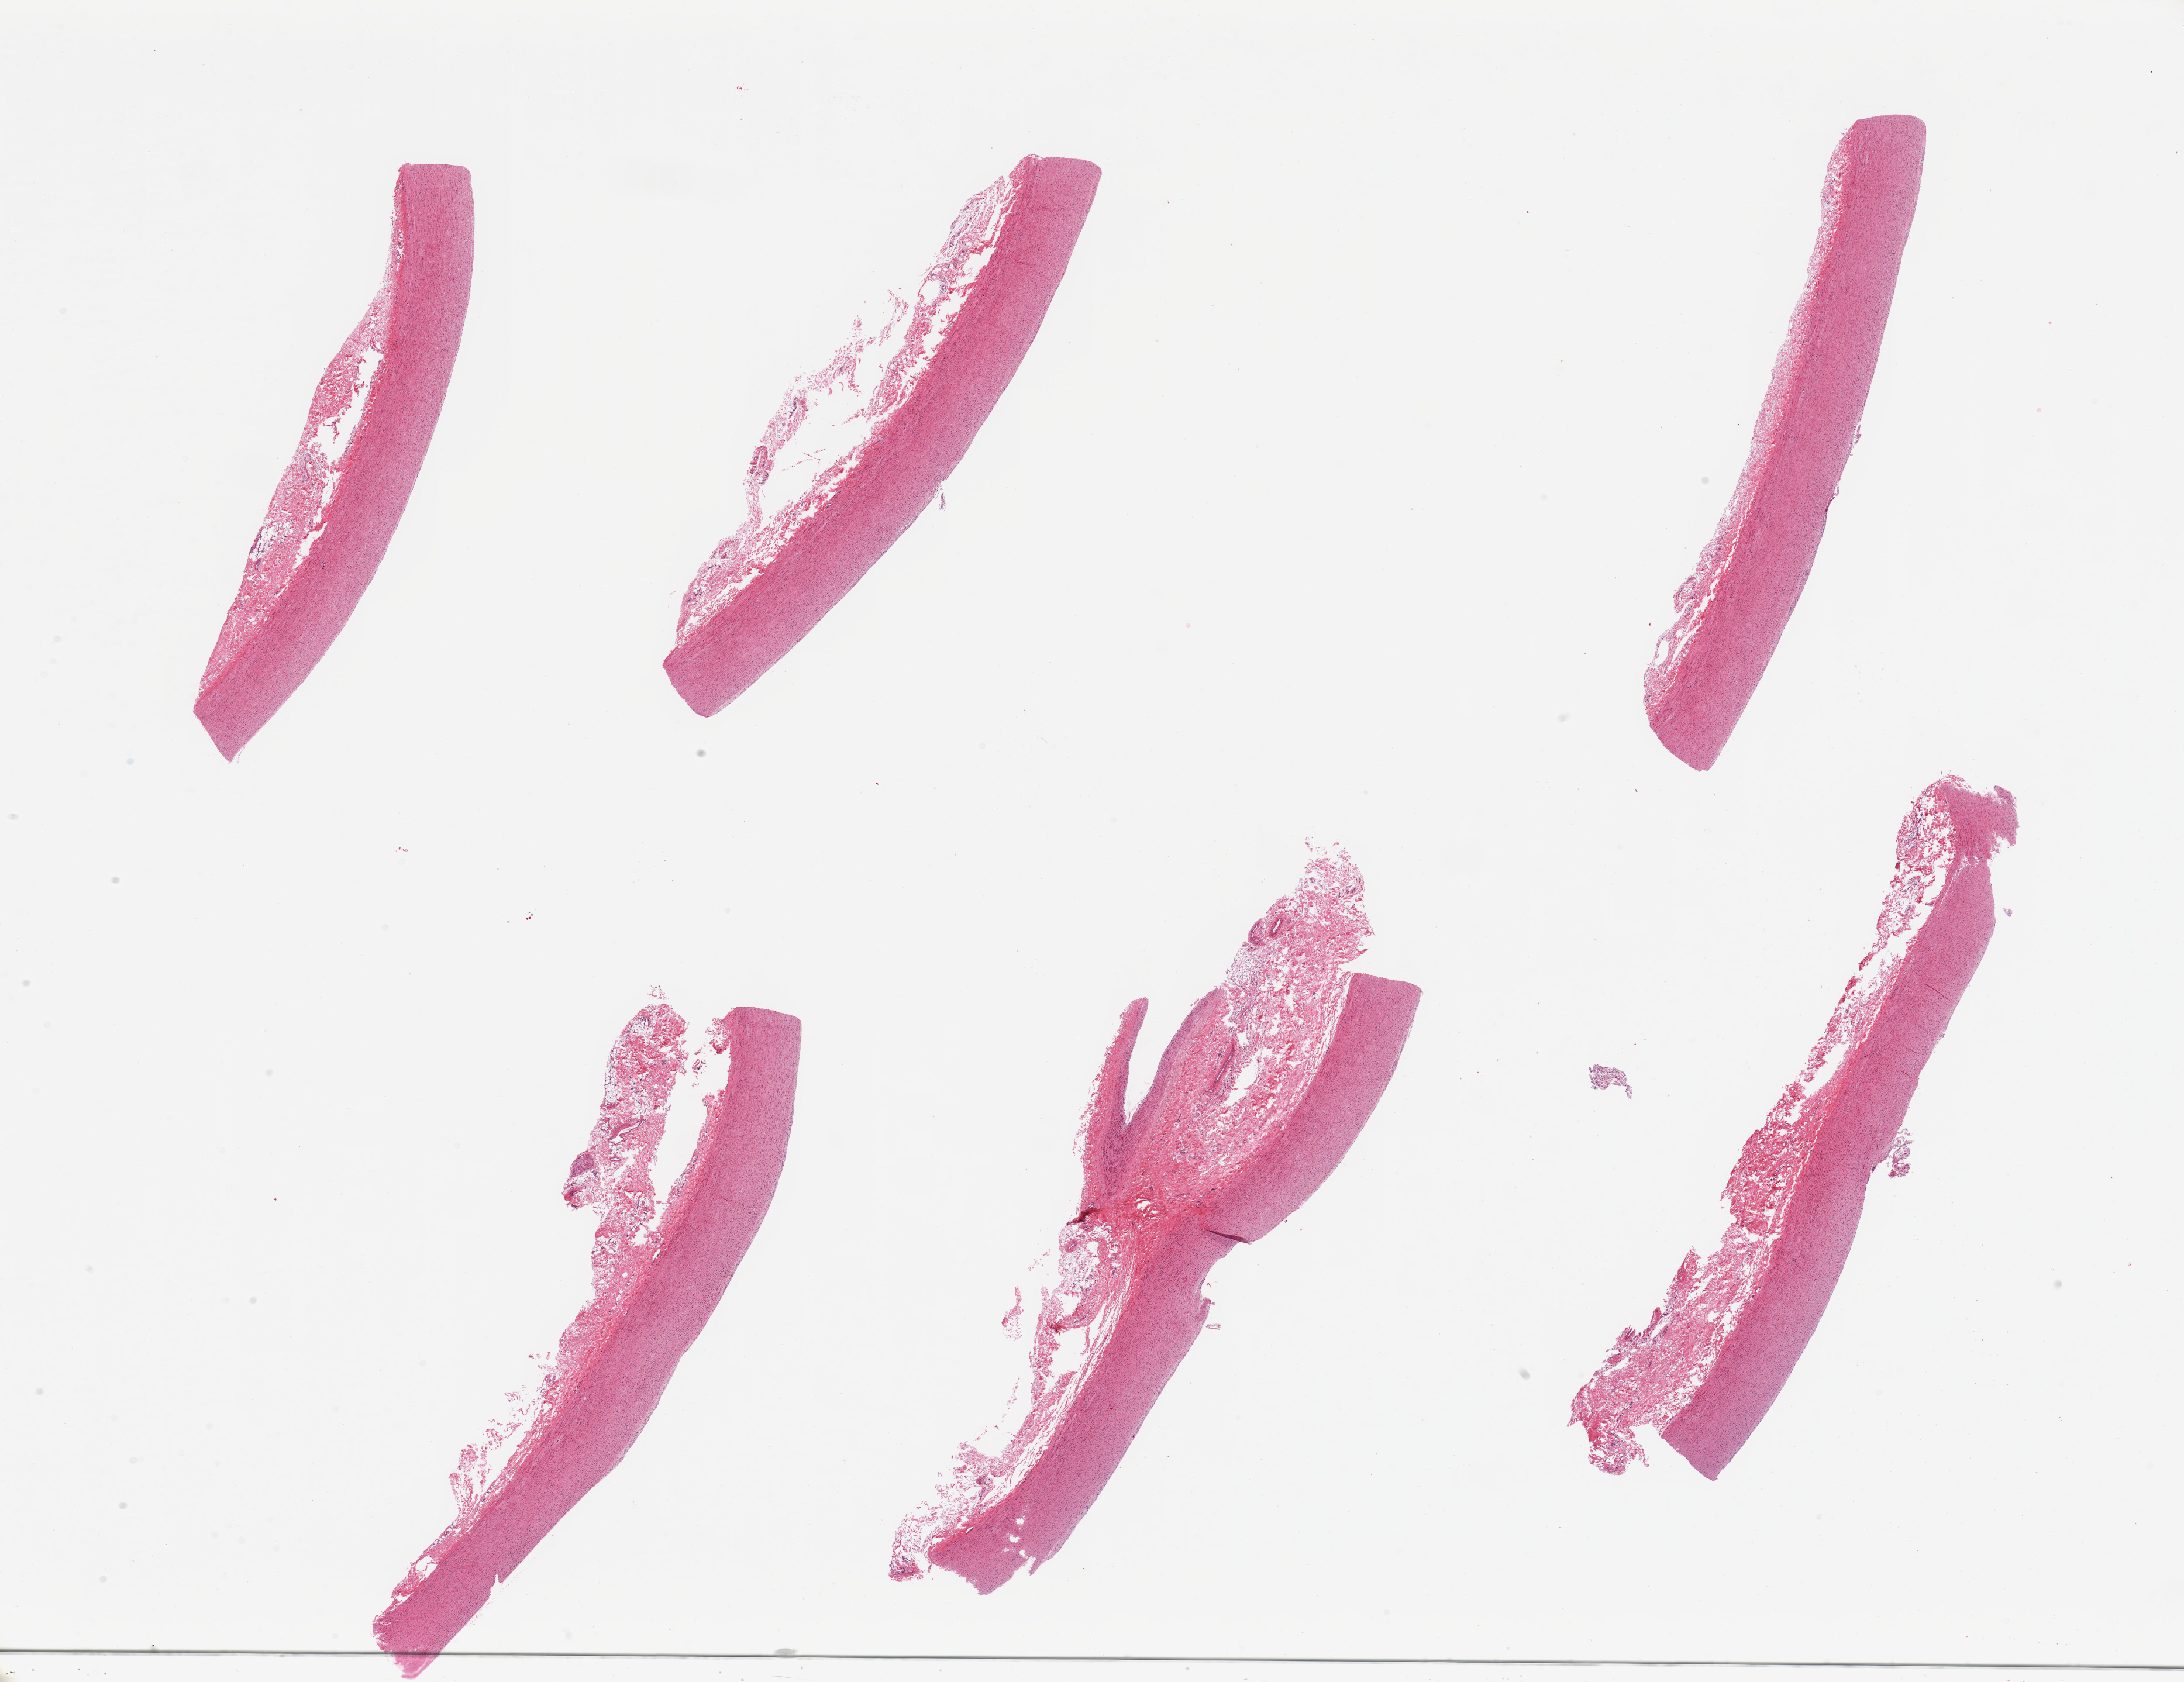
Digitized H&E-stained section, brightfield, a low-resolution overview of the entire scanned area, about 29.5 x 22.7 mm. PAXgene-fixed, paraffin-embedded tissue. Sampled site (target tissue): aorta. Donor tissue sample. Donor: female.
Review note (as recorded): 6 pieces, adherent serosa up to ~1.5mm.